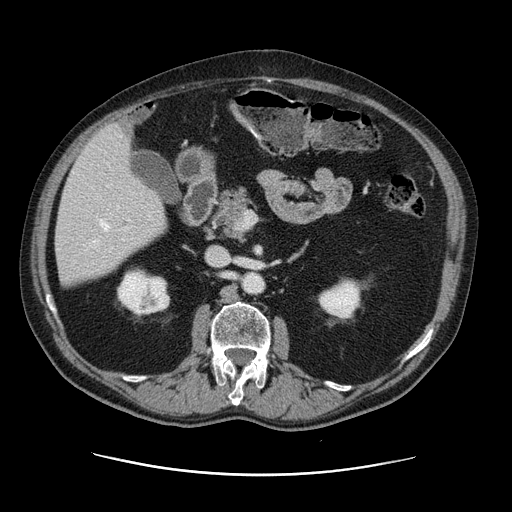
Contrast-enhanced abdominal CT, one axial slice. Position 59 of 141 along the scan axis. Intravenous contrast given. Soft-tissue window (W 400 / L 40 HU). 512 × 512 image matrix. Male patient, age 72 years. Case-level facts recorded for this patient, not image findings: diagnosis: colorectal cancer liver metastases, imaged before liver resection; multiple liver metastases: yes; largest metastasis: 5.4 cm; chemotherapy before resection: yes.
Structures marked on this image (expert manual segmentation):
- hepatic veins: box from (x=94, y=135) to (x=122, y=243) px
- liver: (x=57, y=125)–(x=167, y=287)
- planned liver remnant (the part of the liver to remain after resection): (x=56, y=183)–(x=166, y=287)
- portal vein (with intrahepatic branches): (x=97, y=206)–(x=131, y=243)